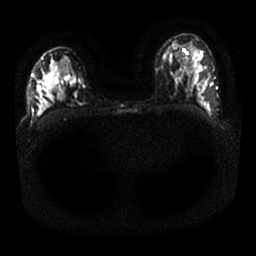
Breast MRI, one axial slice. Position 14 of 25 along the scan axis. Diffusion-weighted series; image 2 of 4 stored at this slice position (different b-values; order by instance number). 1.5 T. 4 mm slice thickness. 256 × 256 image matrix, field of view 330 × 330 mm. Female patient.
Structures marked on this image (expert manual segmentation):
- tumour on diffusion-weighted imaging: bounding box (x1, y1, x2, y2) in pixels: (70, 82, 85, 97)